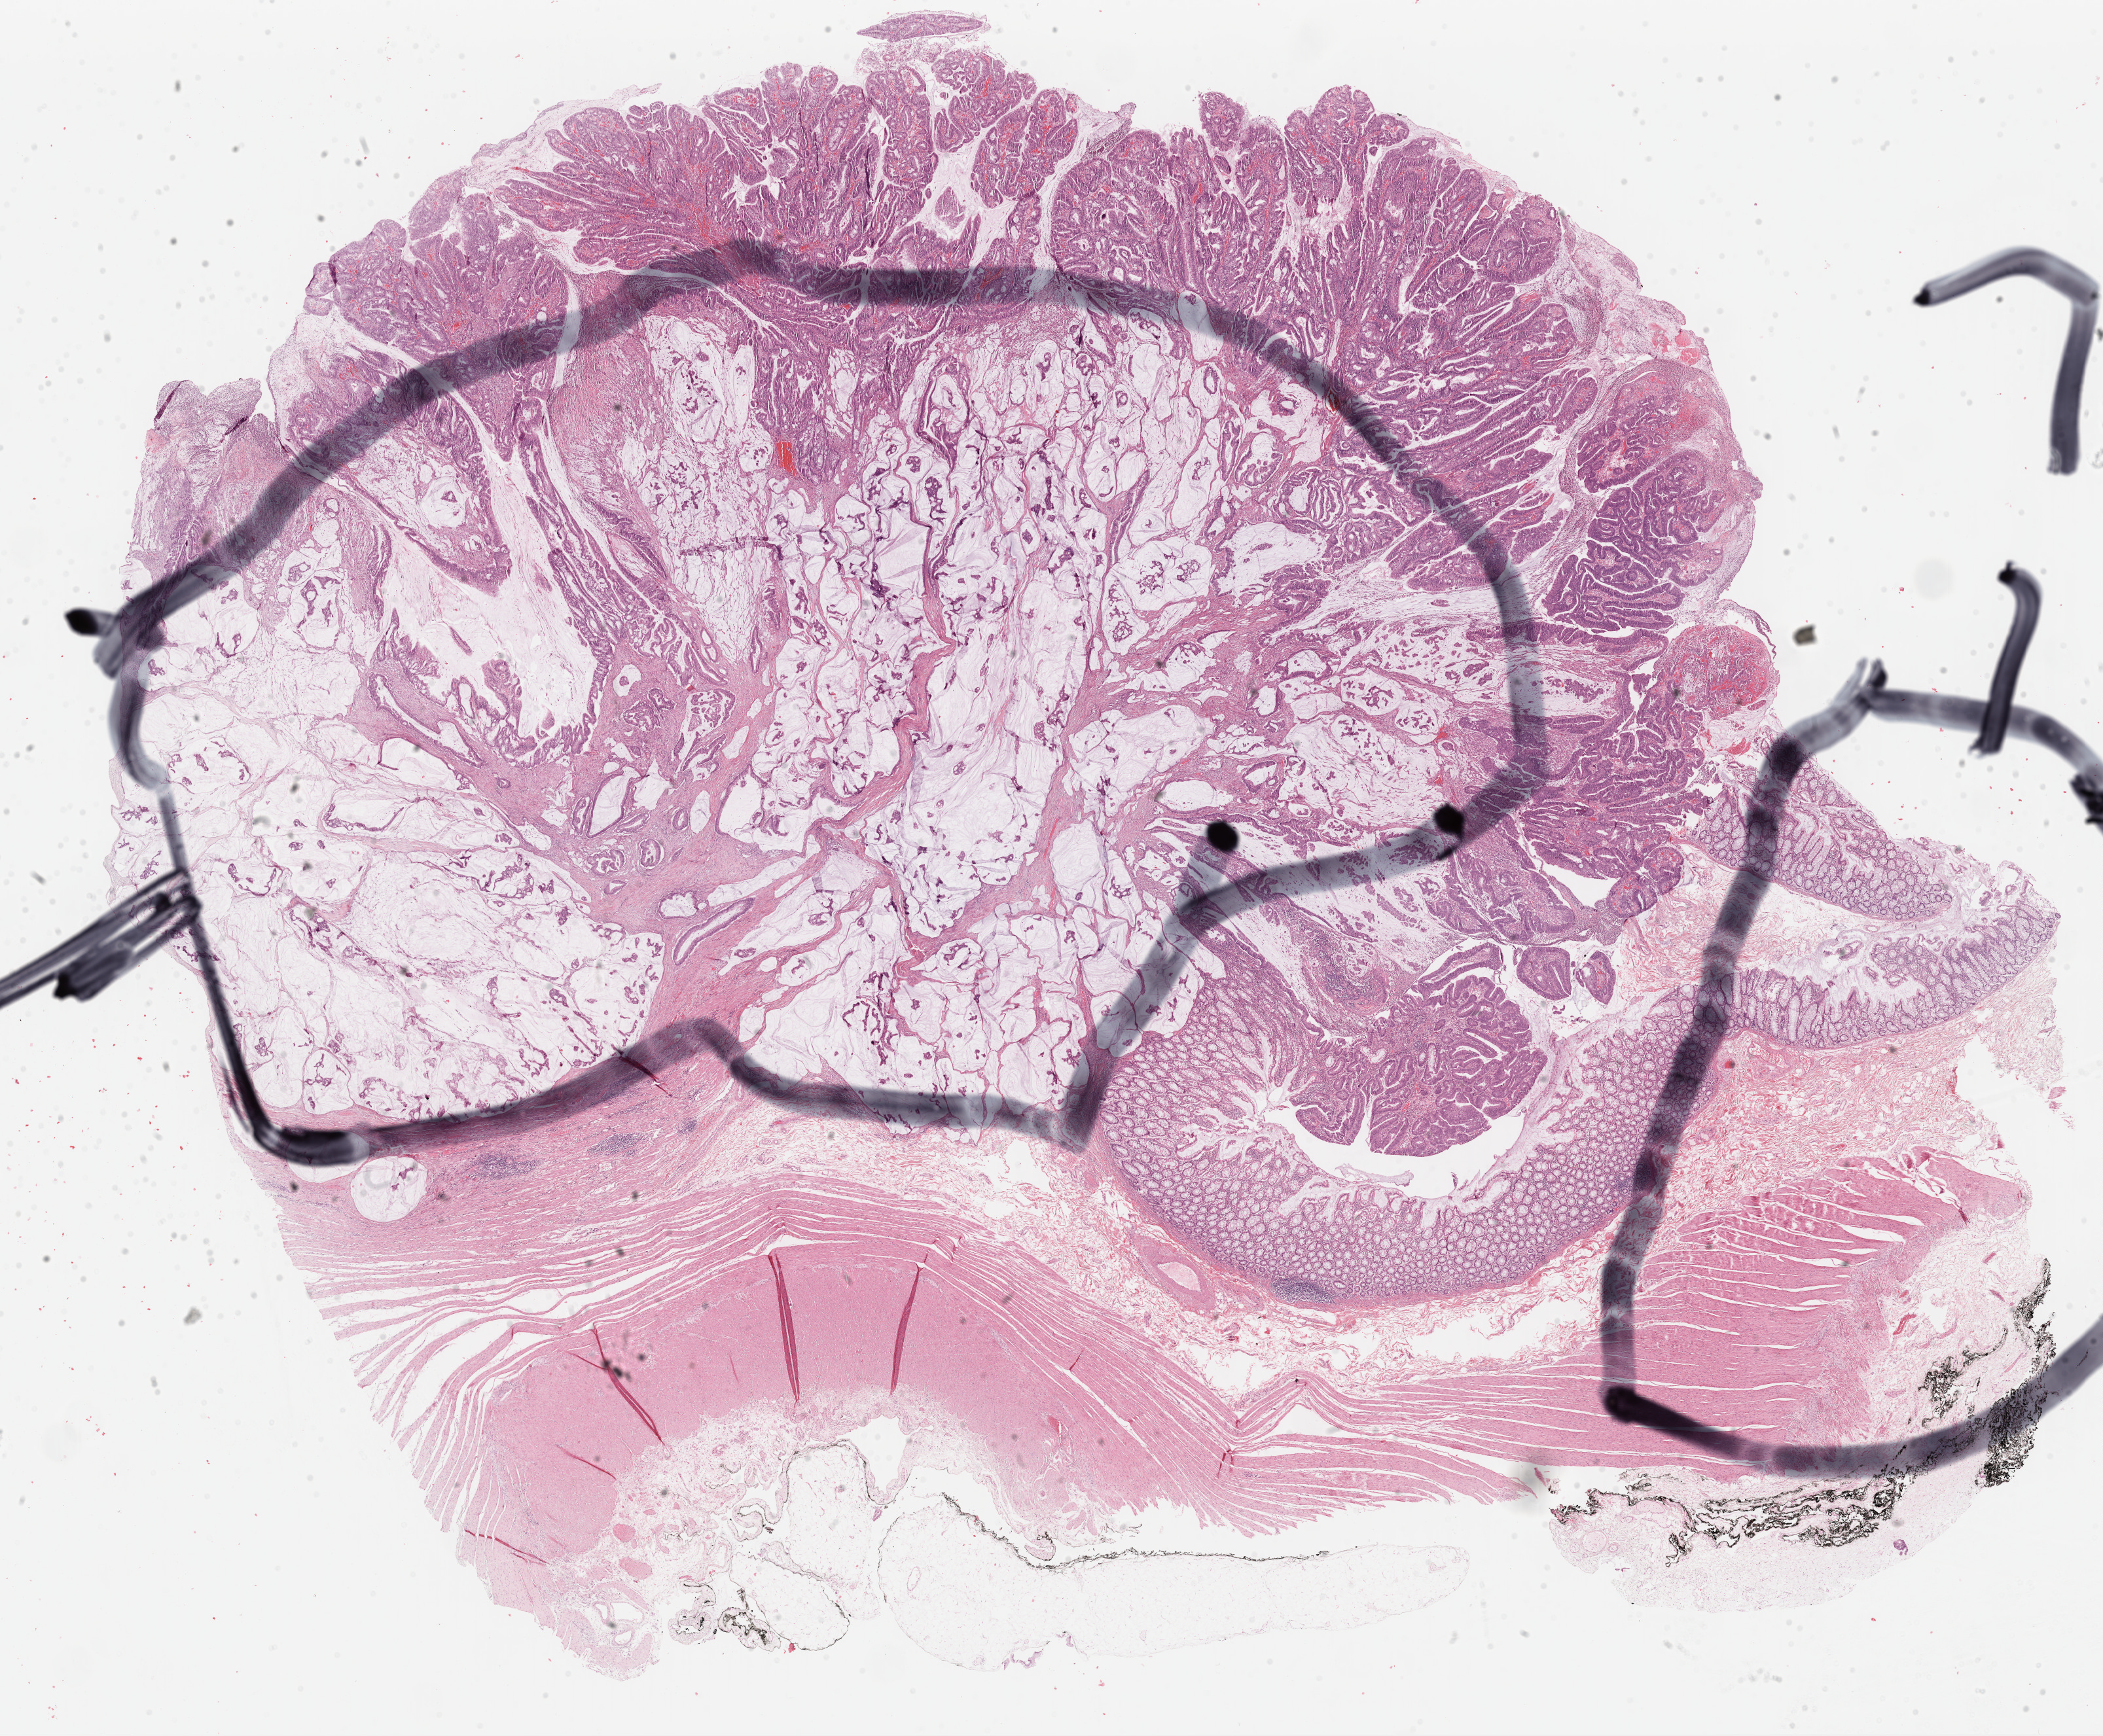
Digitized H&E tissue section (whole slide) — low-resolution overview of the scanned area, about 25.4 x 21.0 mm, formalin-fixed paraffin-embedded (FFPE) diagnostic section, primary tumour sample from the colon. Male, age 75 years at initial diagnosis.
- lymph nodes positive (case pathology): 0 of 17 examined
- TNM: T3 N0 M0
- AJCC pathologic stage: IIA
- diagnosis: Mucinous adenocarcinoma (hepatic flexure of colon)